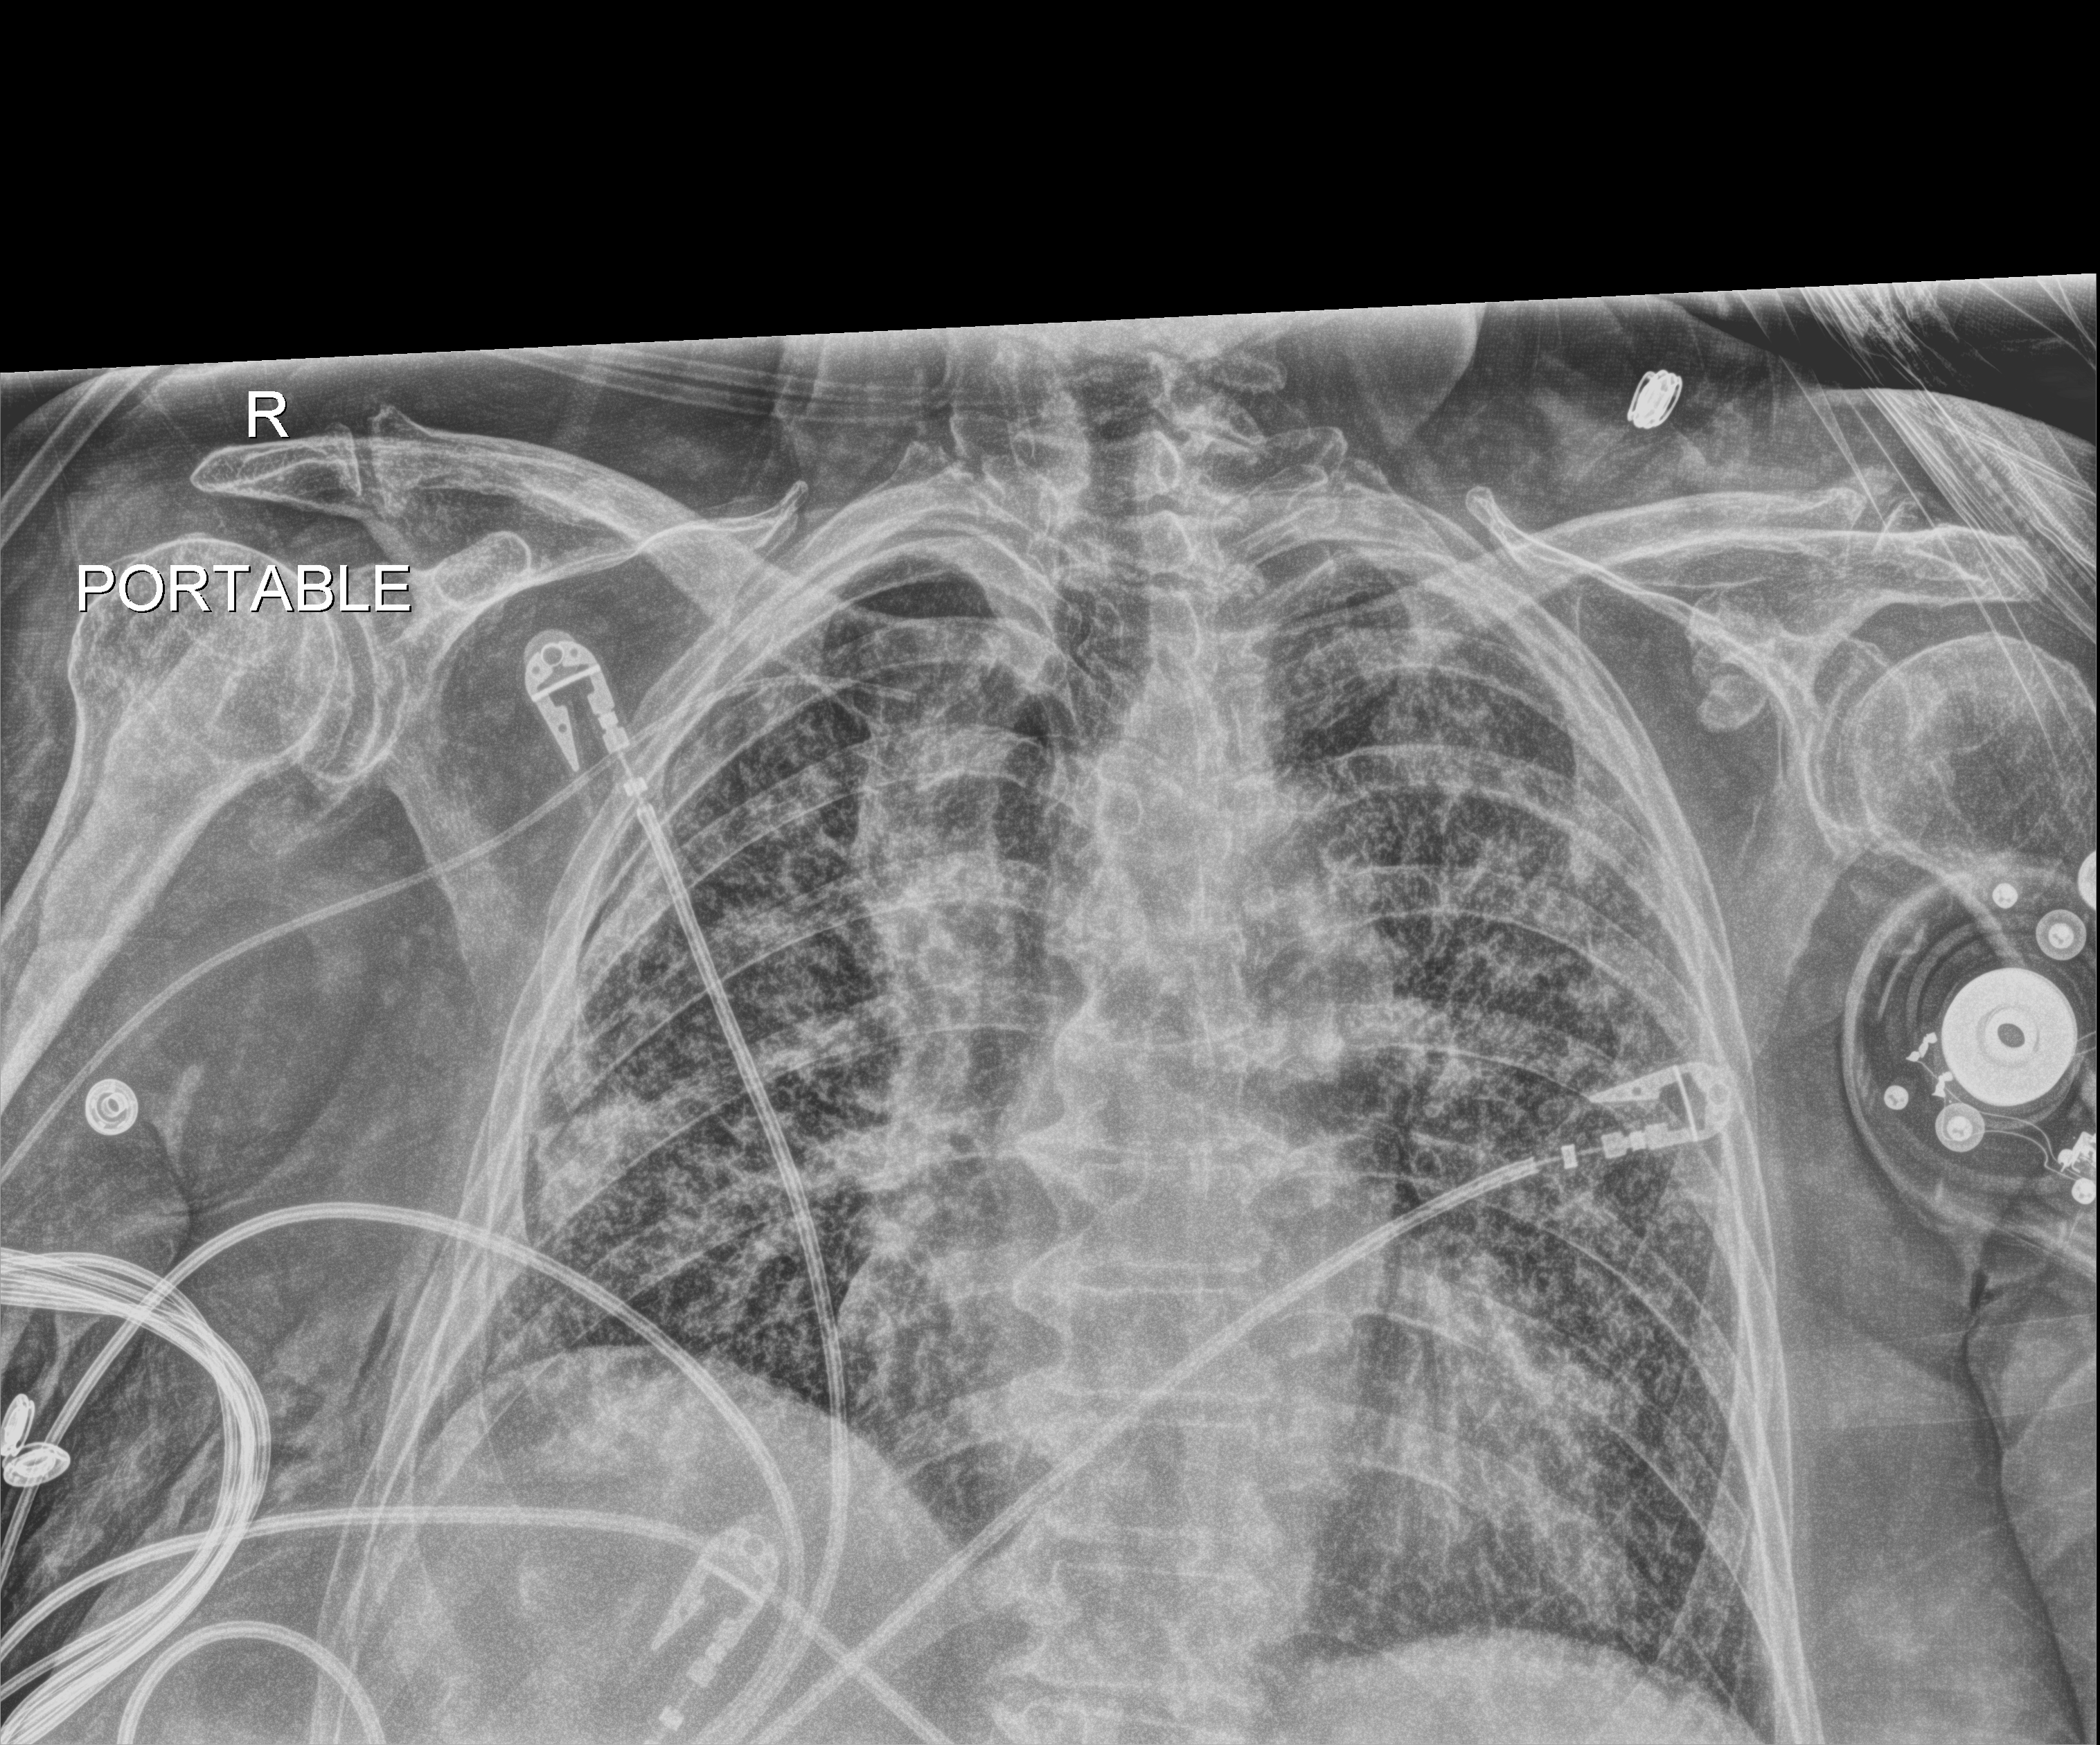
Chest X-ray (portable), anteroposterior (AP) projection. Female patient hospitalised with COVID-19, age 75–90 years.
Hospital-stay facts (about this admission, not read from this image; timing relative to this image not recorded): chronic kidney disease (admission record): no; admitted to intensive care during this hospital stay: no.